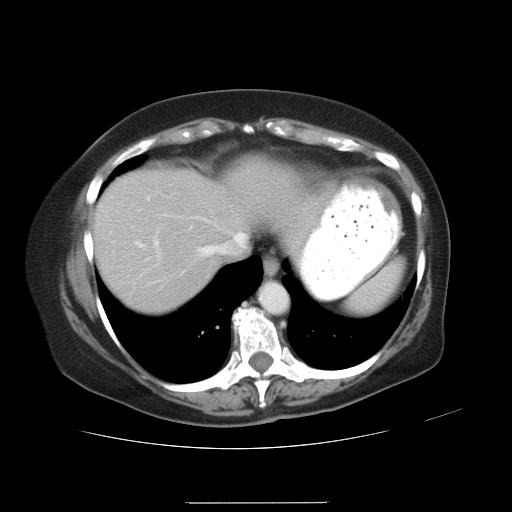
Contrast-enhanced abdominal CT, one axial slice. Slice 26 of 32 in the series (ordered by position). Reconstruction kernel STANDARD. 120 kVp. Intravenous contrast given. Soft-tissue window (W 400 / L 40 HU). 7.5 mm slice thickness. 512 × 512 image matrix, field of view 386 × 386 mm. Female patient, age 65 years. Case-level facts recorded for this patient, not image findings: diagnosis: colorectal cancer liver metastases, imaged before liver resection; multiple liver metastases: yes; largest metastasis: 1.7 cm; chemotherapy before resection: no.
Annotated regions visible in this slice (manually delineated by an expert):
- hepatic veins: bounding box [x1, y1, x2, y2] px = [149, 216, 247, 285]
- liver: [94, 160, 311, 314]
- planned liver remnant (the part of the liver to remain after resection): [94, 170, 242, 314]
- portal vein (with intrahepatic branches): [137, 231, 159, 249]